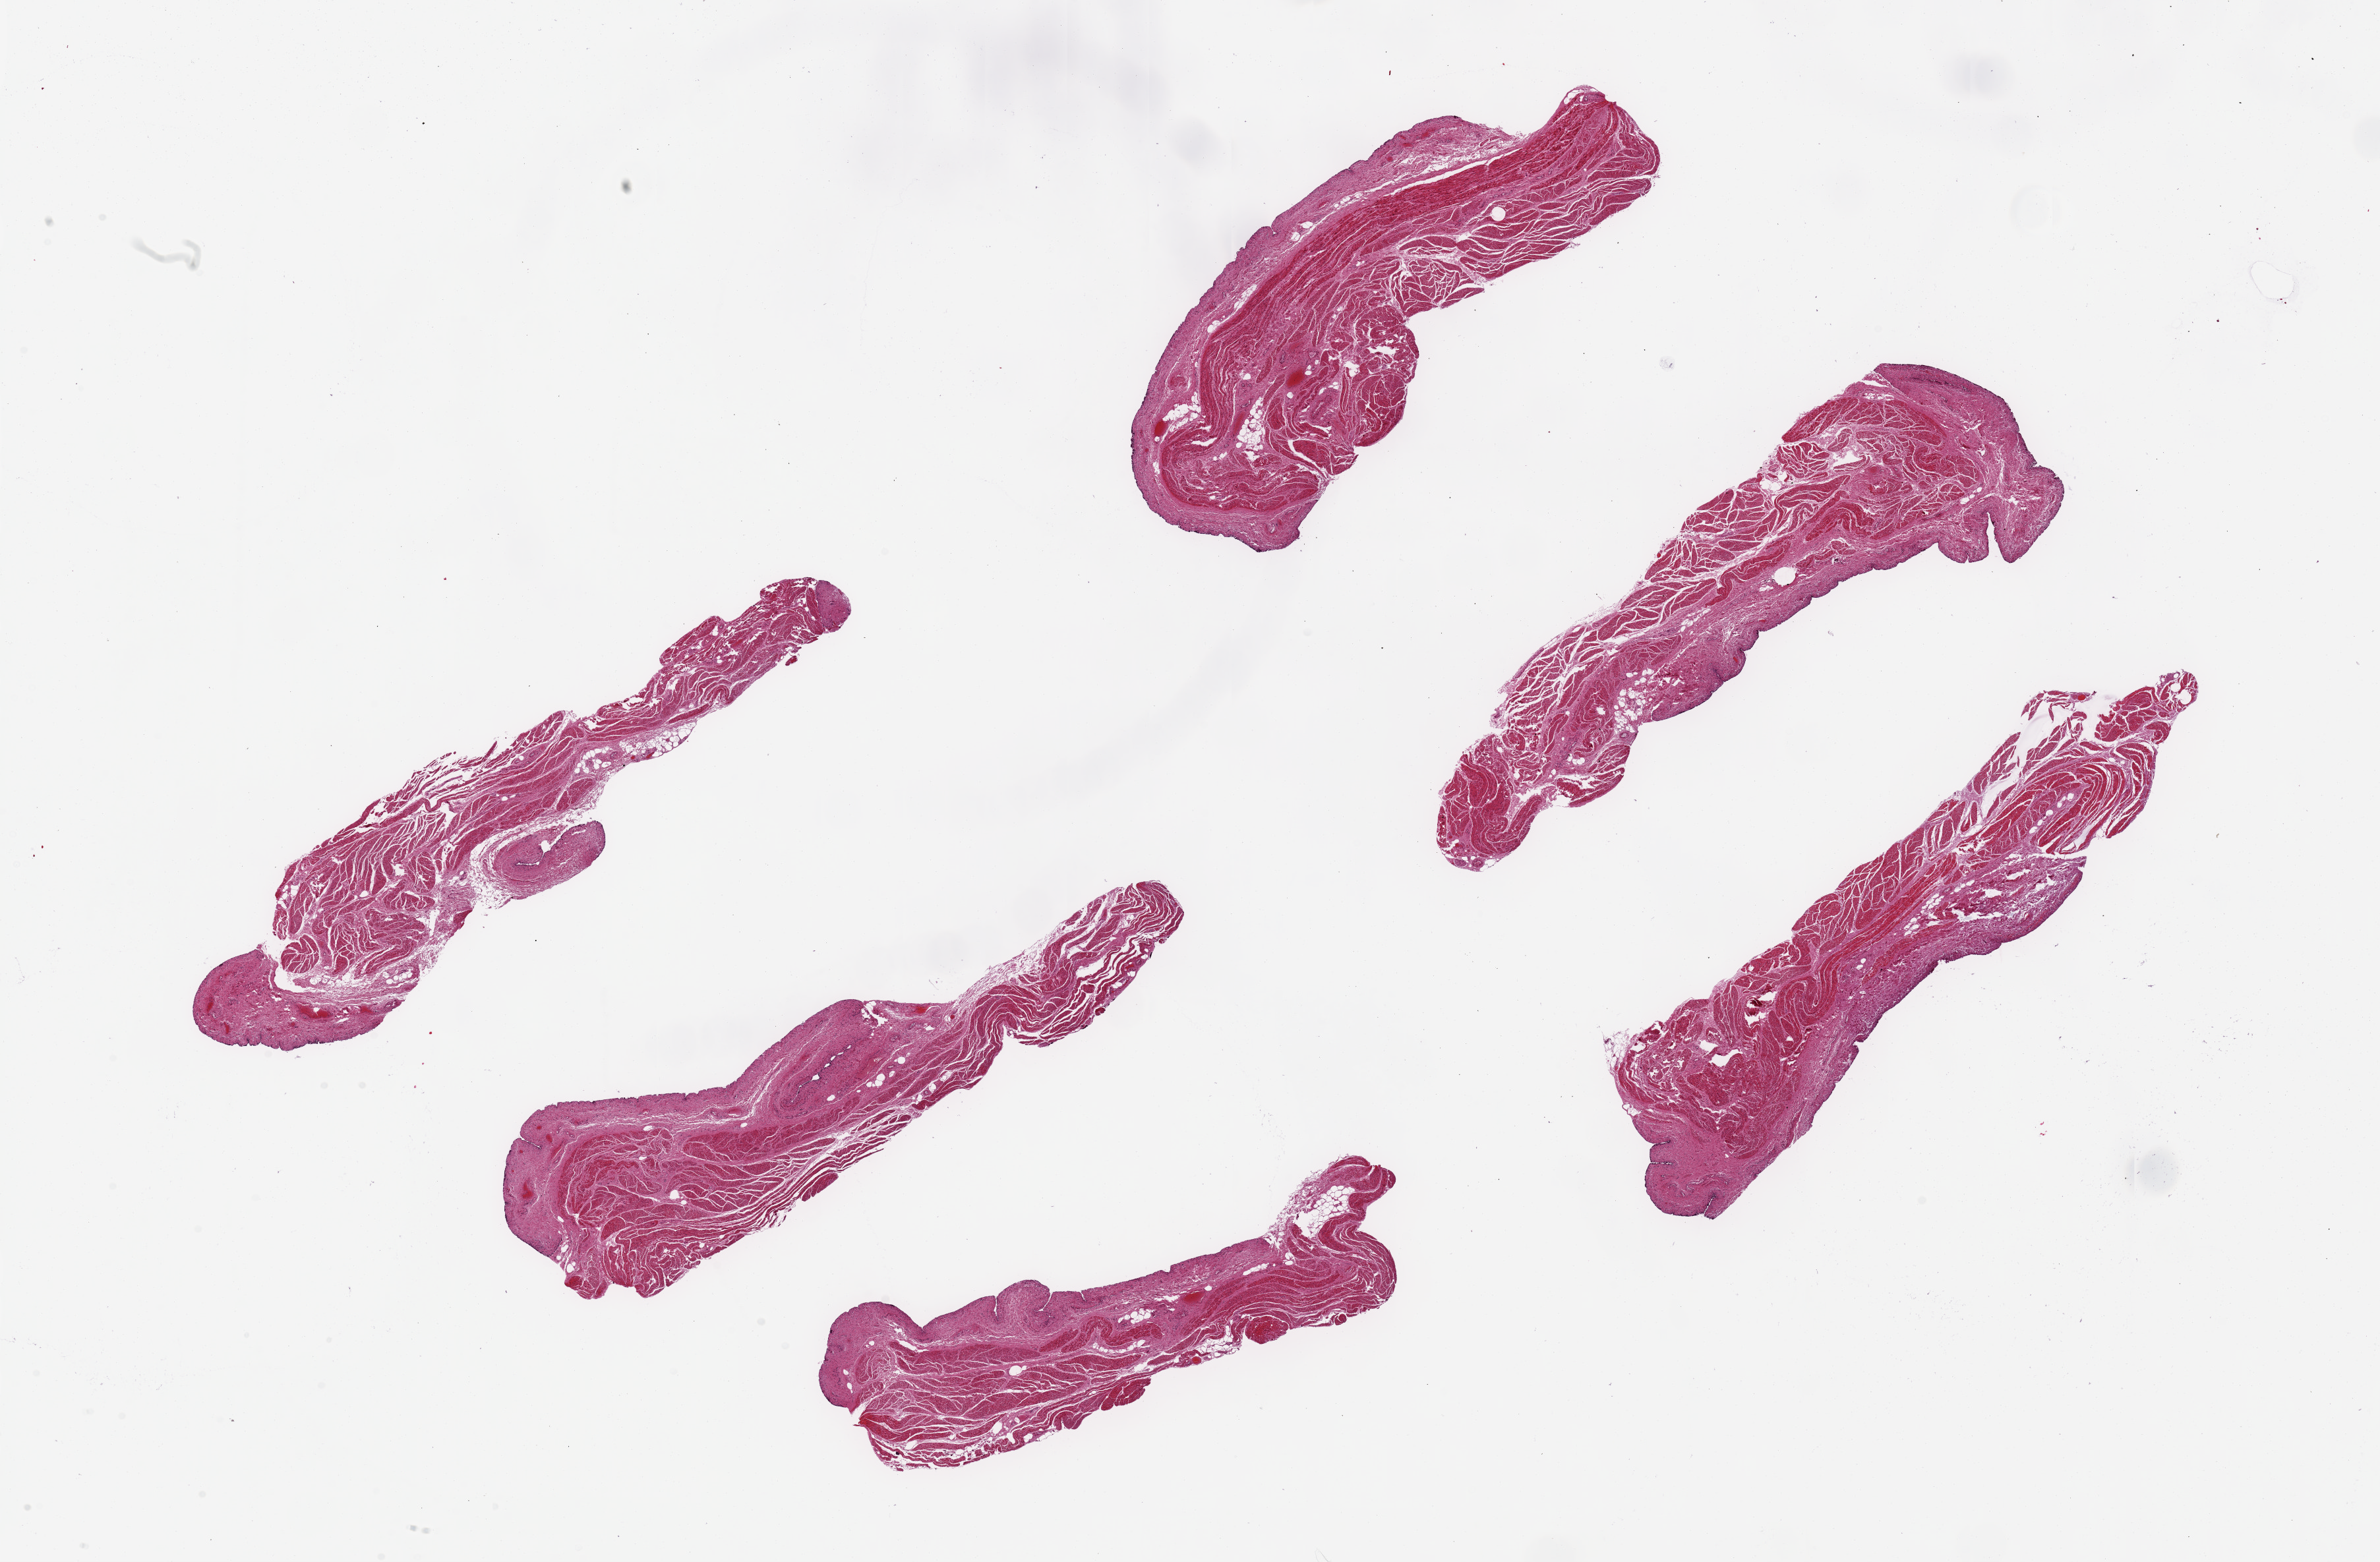
Whole-slide image, haematoxylin and eosin stain — a low-resolution overview of the entire scanned area, about 28.5 x 18.7 mm (acquisition: 20x scan), PAXgene-fixed, paraffin-embedded tissue, sampled site (target tissue): urinary bladder, donor tissue sample. Male donor.
Reviewer comment on this tissue sample: 4 pieces,~8x2.5 mm; surface largely sloughed.